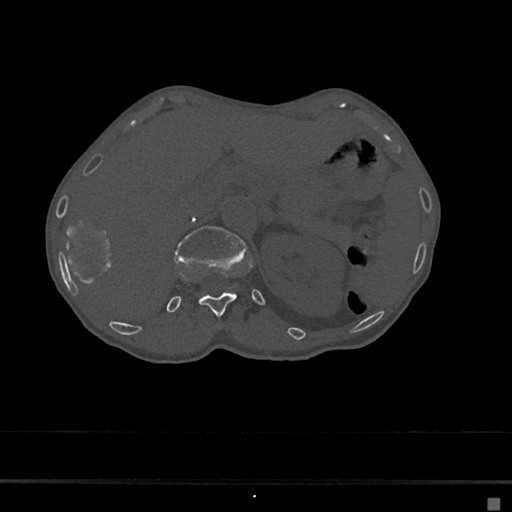
CT including the spine, one axial slice; slice 110 of 797 in the series (ordered by position); 120 kVp; bone window (W 1800 / L 400 HU); 0.5 mm slice thickness; 512 × 512 image matrix, field of view 360 × 360 mm. Female patient, age 68 years. From the clinical record (not read from this slice): primary cancer: renal.
Annotated regions visible in this slice (semi-automatic segmentation, software-assisted and operator-edited):
- L1 vertebra: bounding box [x1, y1, x2, y2] px = [174, 226, 248, 263]
- T12 vertebra: [198, 268, 237, 316]